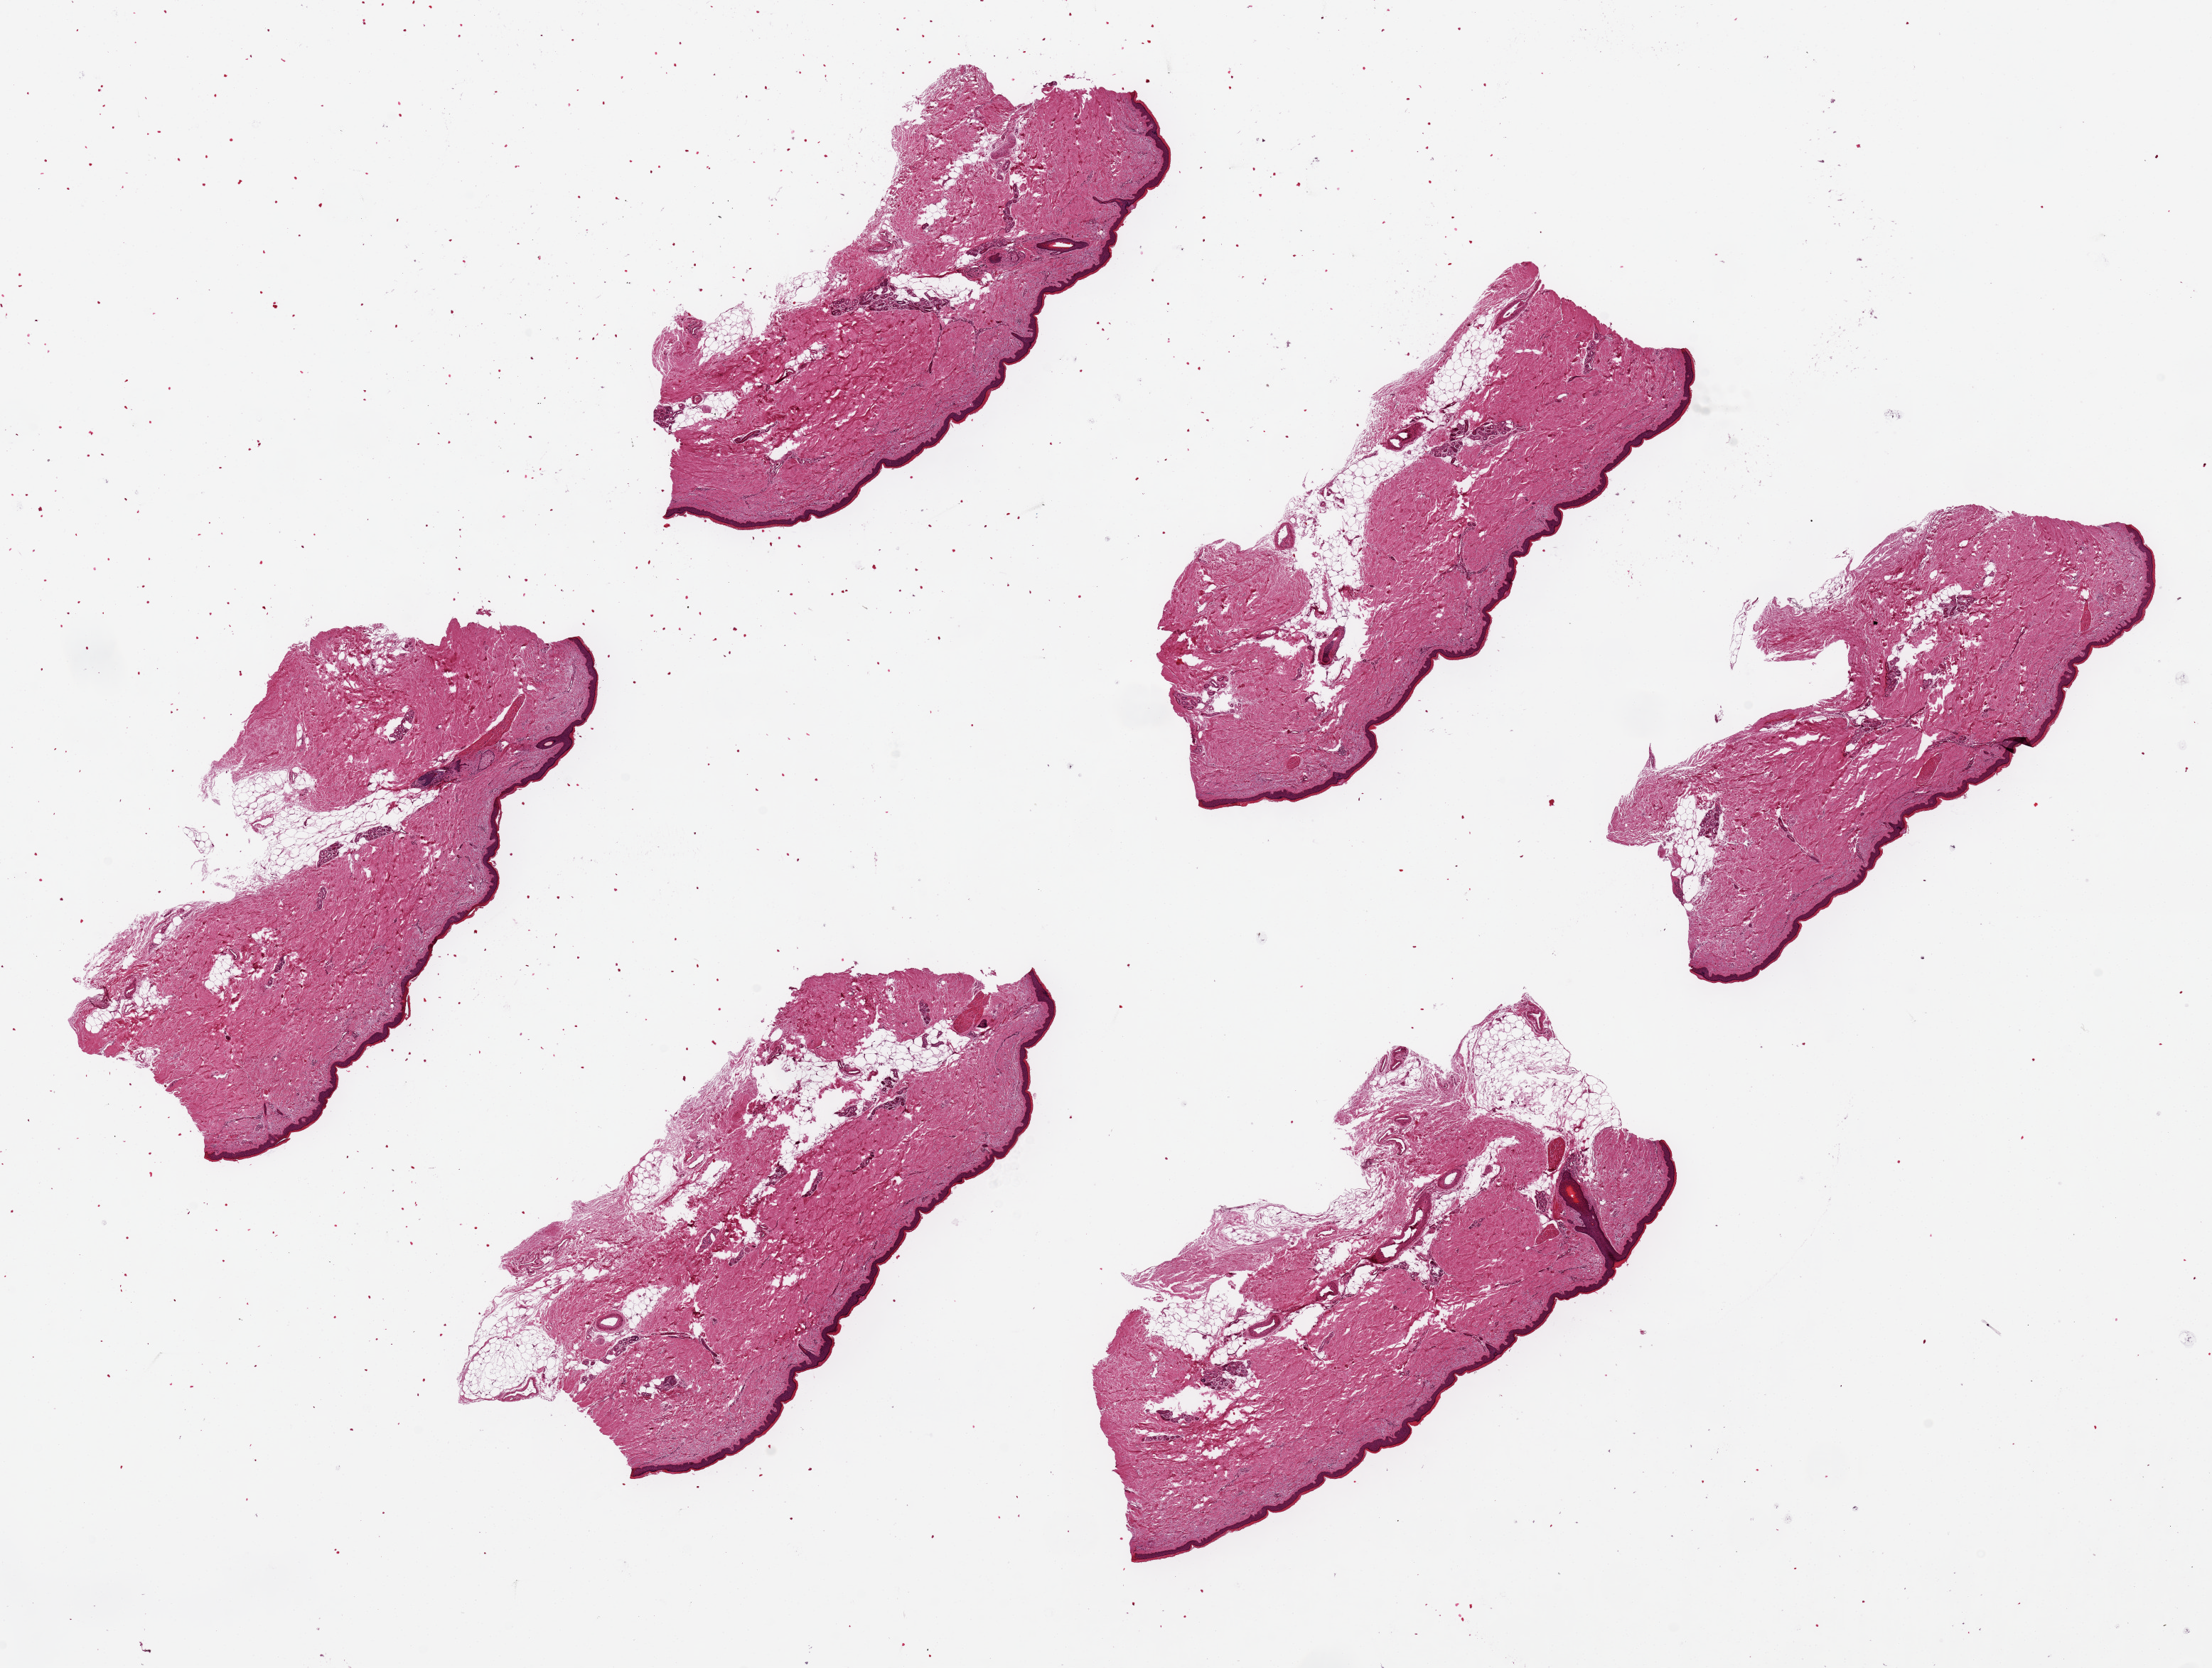
Digitized haematoxylin and eosin-stained section, whole scanned area (about 24.6 x 18.6 mm) shown as a low-resolution overview, PAXgene-fixed, paraffin-embedded tissue, sampled site (target tissue): skin of lower leg, donor tissue sample.
Review note (as recorded): 6 pieces, 6xx3mm. Squamous mucosa is ~2-3% of thickness.